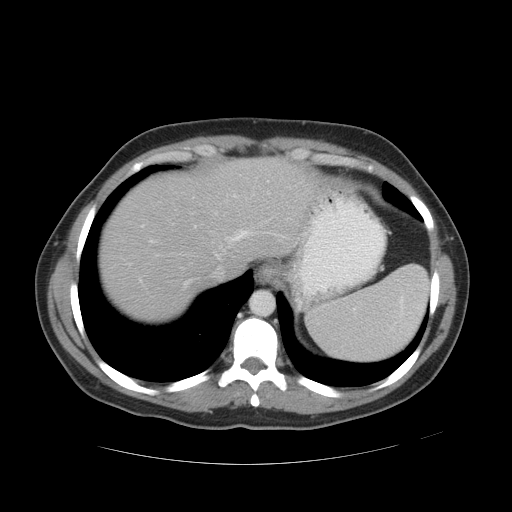
Contrast-enhanced abdominal CT, one axial slice. Position 42 of 49 along the scan axis. Reconstruction kernel STANDARD. 120 kVp. Intravenous contrast given. Soft-tissue window (W 400 / L 40 HU). 5 mm slice thickness. 512 × 512 image matrix. Male patient, age 42 years. Case-level facts recorded for this patient, not image findings: diagnosis: colorectal cancer liver metastases, imaged before liver resection.
Annotated regions visible in this slice (expert manual segmentation):
- hepatic veins: bounding box [x1, y1, x2, y2] px = [149, 195, 285, 288]
- liver: [100, 159, 313, 320]
- planned liver remnant (the part of the liver to remain after resection): [100, 159, 313, 320]
- portal vein (with intrahepatic branches): [129, 225, 144, 282]